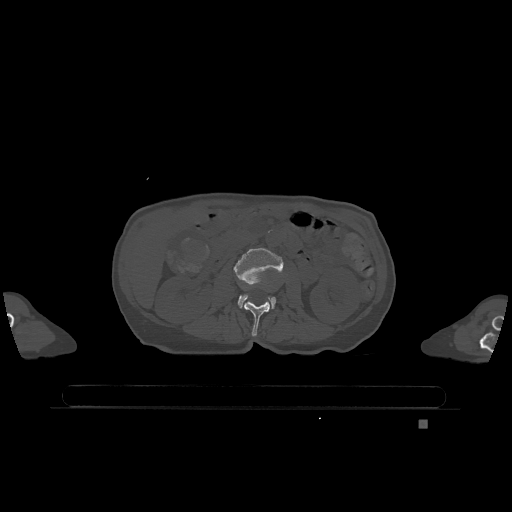
CT including the spine, one axial slice; slice 392 of 1317 in the series (ordered by position); bone window (W 1800 / L 400 HU); 512 × 512 image matrix, field of view 500 × 500 mm. Female patient, age 74 years. From the clinical record (not read from this slice): primary cancer: lung; vertebrae with lytic lesions (as recorded): T1, T4, T5, T6, L4, L5.
Structures marked on this image (semi-automatically segmented with operator editing):
- L2 vertebra: bounding box <244,301,270,336> (left, top, right, bottom; pixels)
- L3 vertebra: <234,248,283,308>